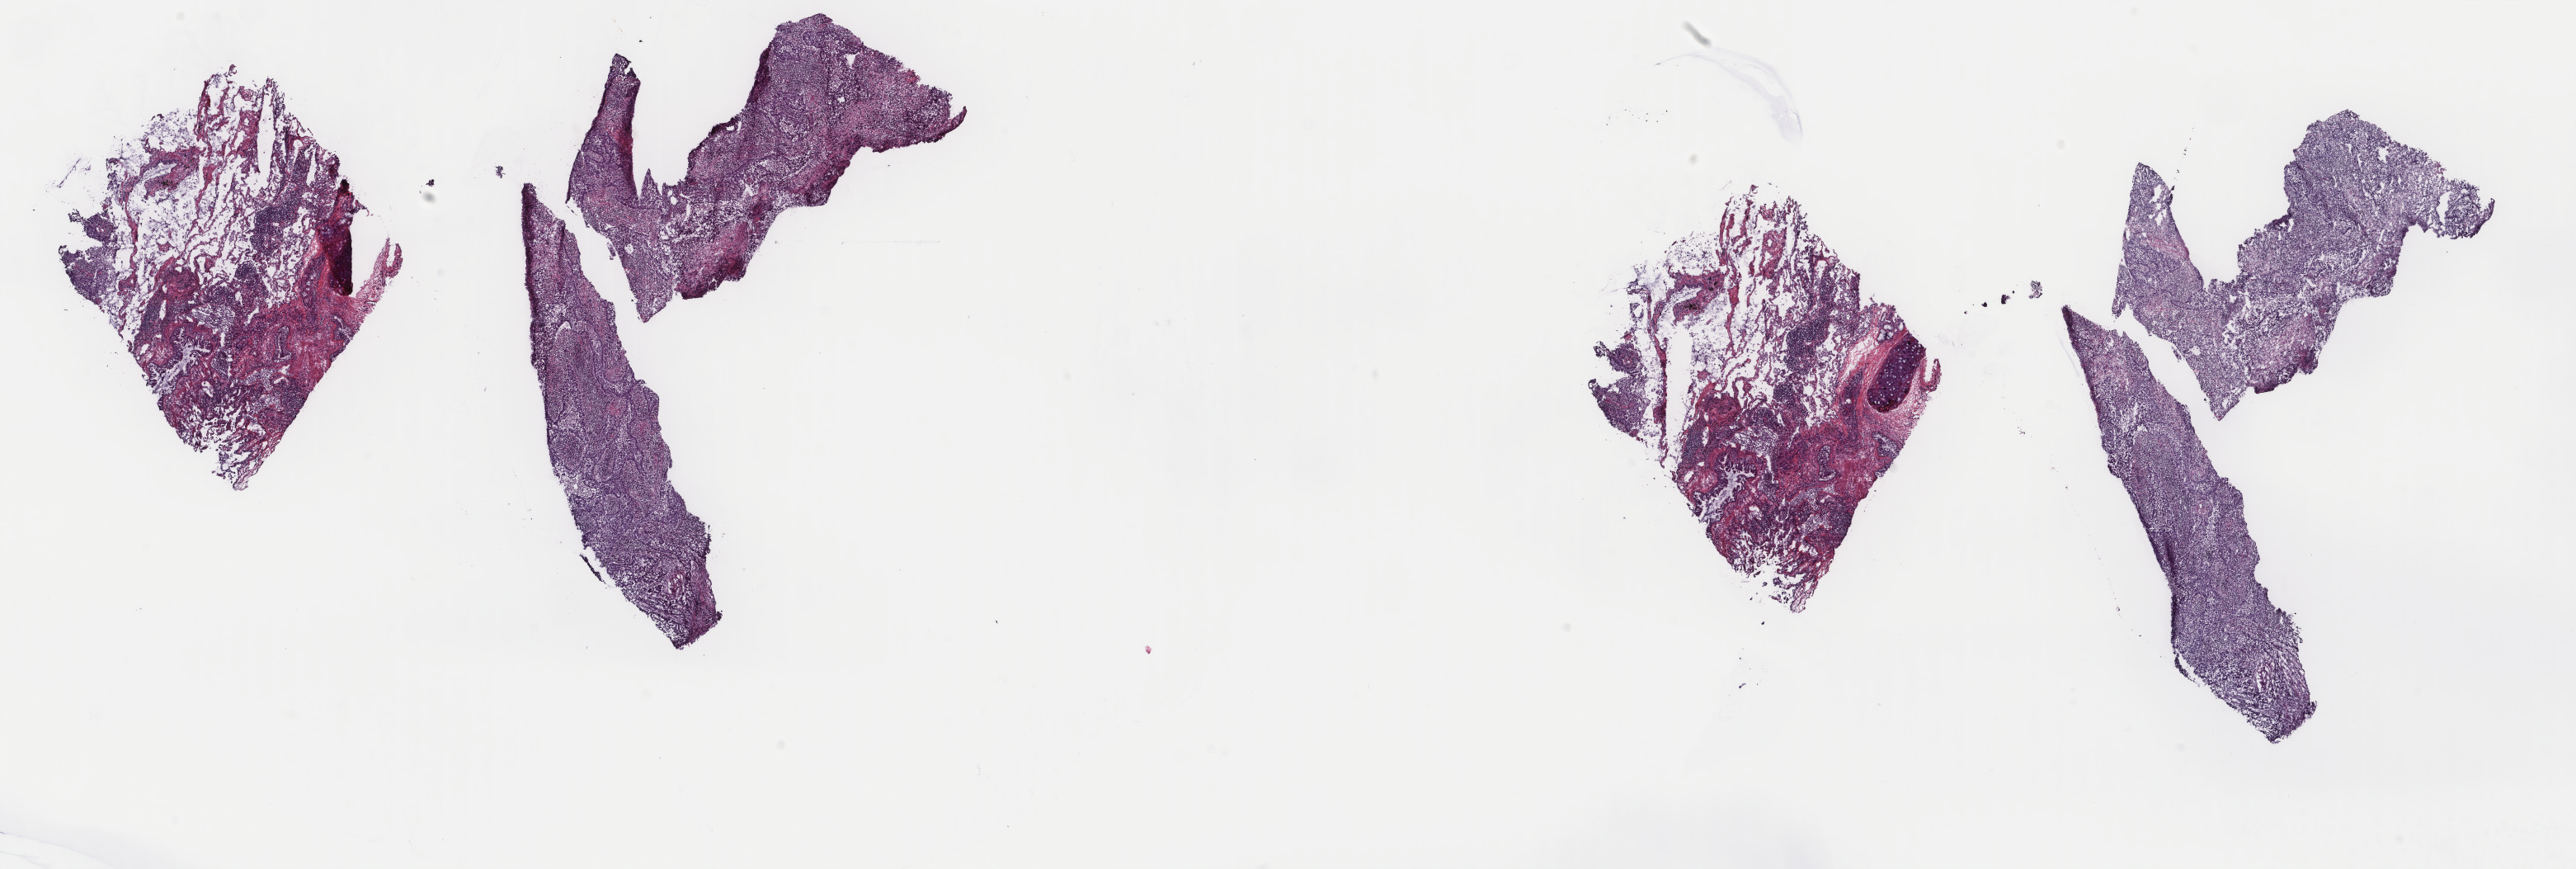
H&E whole-slide image, a low-resolution overview of the entire scanned area, about 24.8 x 8.4 mm (slide scanned at 40x), frozen section, sample: primary tumour, lung. Female, age 62 years at initial diagnosis. Slide review estimates, as recorded: tumour cells 60%, tumour nuclei 60%, normal cells 30%, stromal cells 10%, necrosis 0%. Infiltration values recorded for this section: lymphocyte infiltration 0%, monocyte infiltration 0%, neutrophil infiltration 0%.
AJCC pathologic stage: IA (6th edition). Histologic diagnosis: Signet ring cell carcinoma. TNM: T1 N0 M0. Laterality: right.